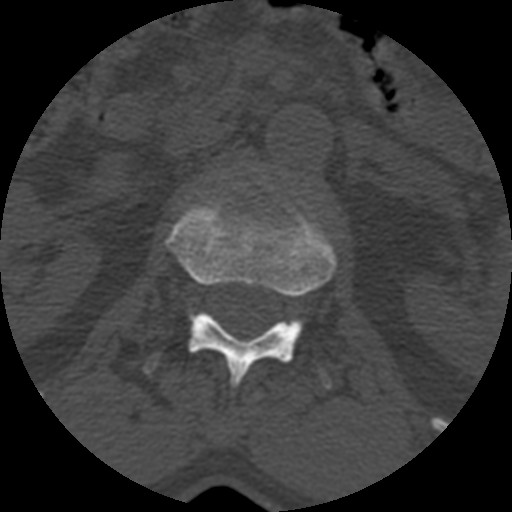
CT including the spine, one axial slice. Slice 357 of 399 in the series (ordered by position). 120 kVp. Bone window (W 1800 / L 400 HU). 1.25 mm slice thickness. 512 × 512 image matrix, field of view 160 × 160 mm. Patient age 71 years. Case-level facts recorded for this patient, not image findings: primary cancer: prostate.
Annotated regions visible in this slice (semi-automatic segmentation, software-assisted and operator-edited):
- L1 vertebra: bounding box <151,201,335,388> (left, top, right, bottom; pixels)